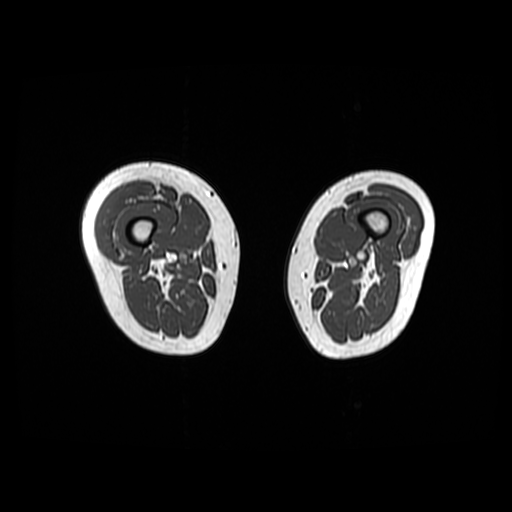
MRI of an extremity soft-tissue mass, one axial slice. Position 11 of 48 along the scan axis. 6 mm slice thickness. 512 × 512 image matrix. Female patient. Case-level facts recorded for this patient, not image findings: histological type: pleiomorphic undifferentiated sarcoma; grade: high; site of the primary tumour: right quadricep.
Annotated regions visible in this slice (manually delineated by an expert):
- gross tumour volume including surrounding oedema: bounding box <97,182,157,240> (left, top, right, bottom; pixels)